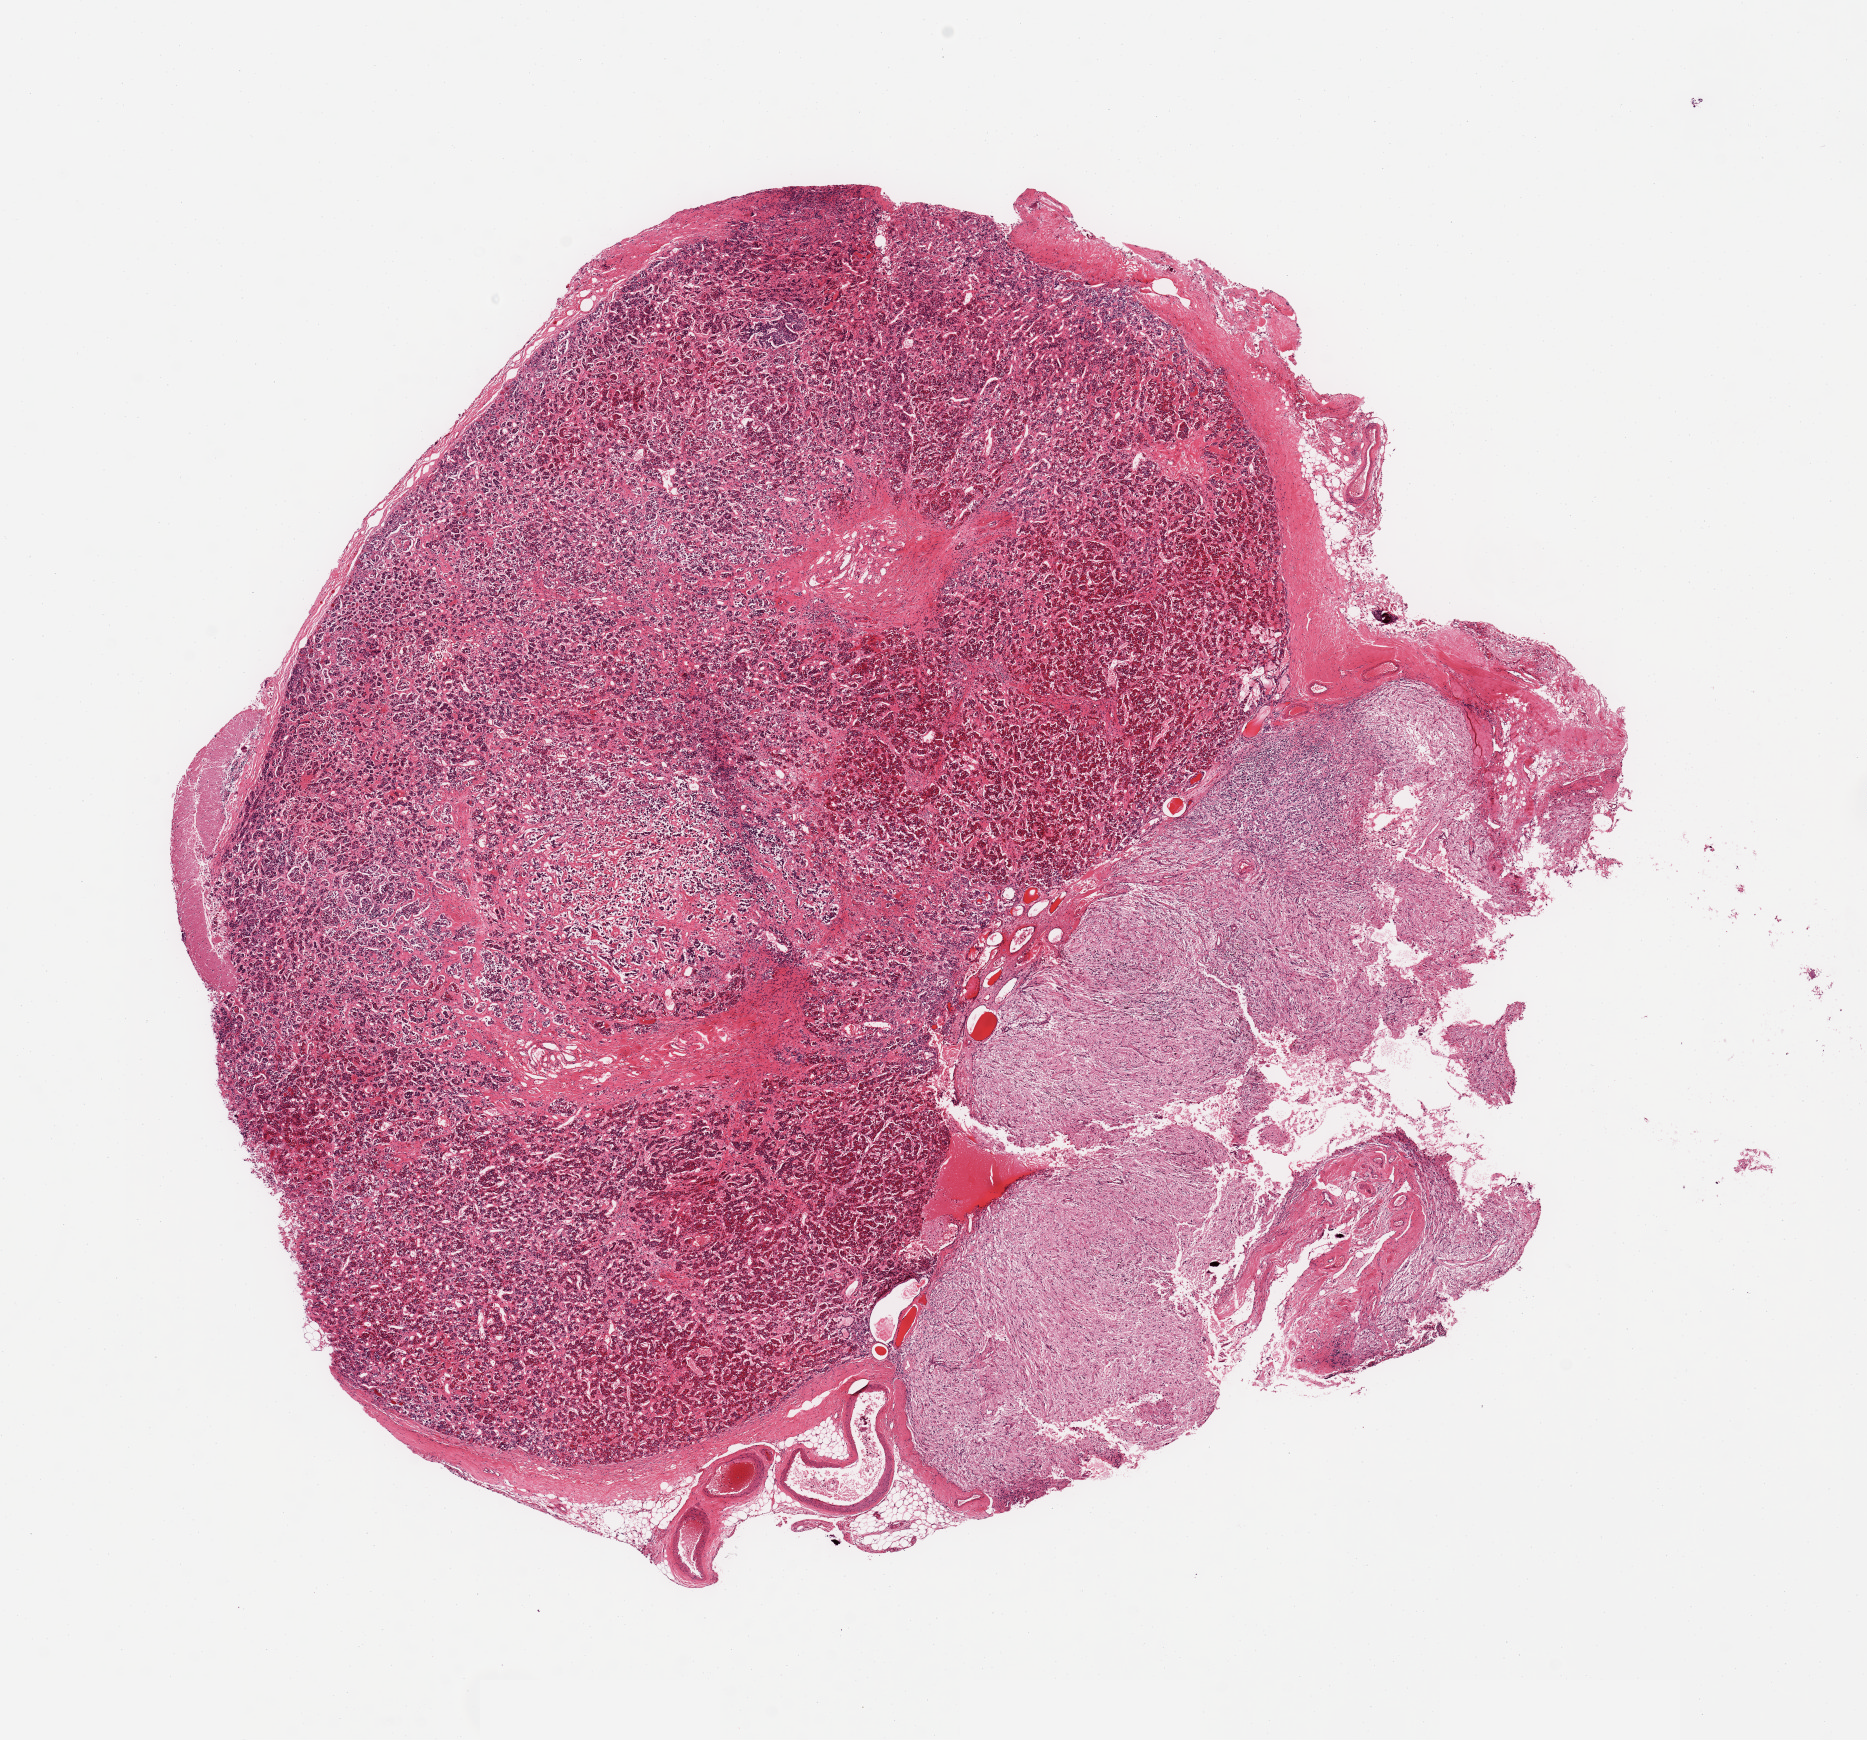
Whole-slide image, haematoxylin and eosin stain — a low-resolution overview of the entire scanned area, about 14.8 x 13.8 mm; PAXgene-fixed, paraffin-embedded tissue; section of pituitary (target tissue); donor tissue sample.
- pathologist's review note for this sample: 1 piece, ~70% adenohypophysis; 7x4mm fragment of neurohypophysis is ~30%